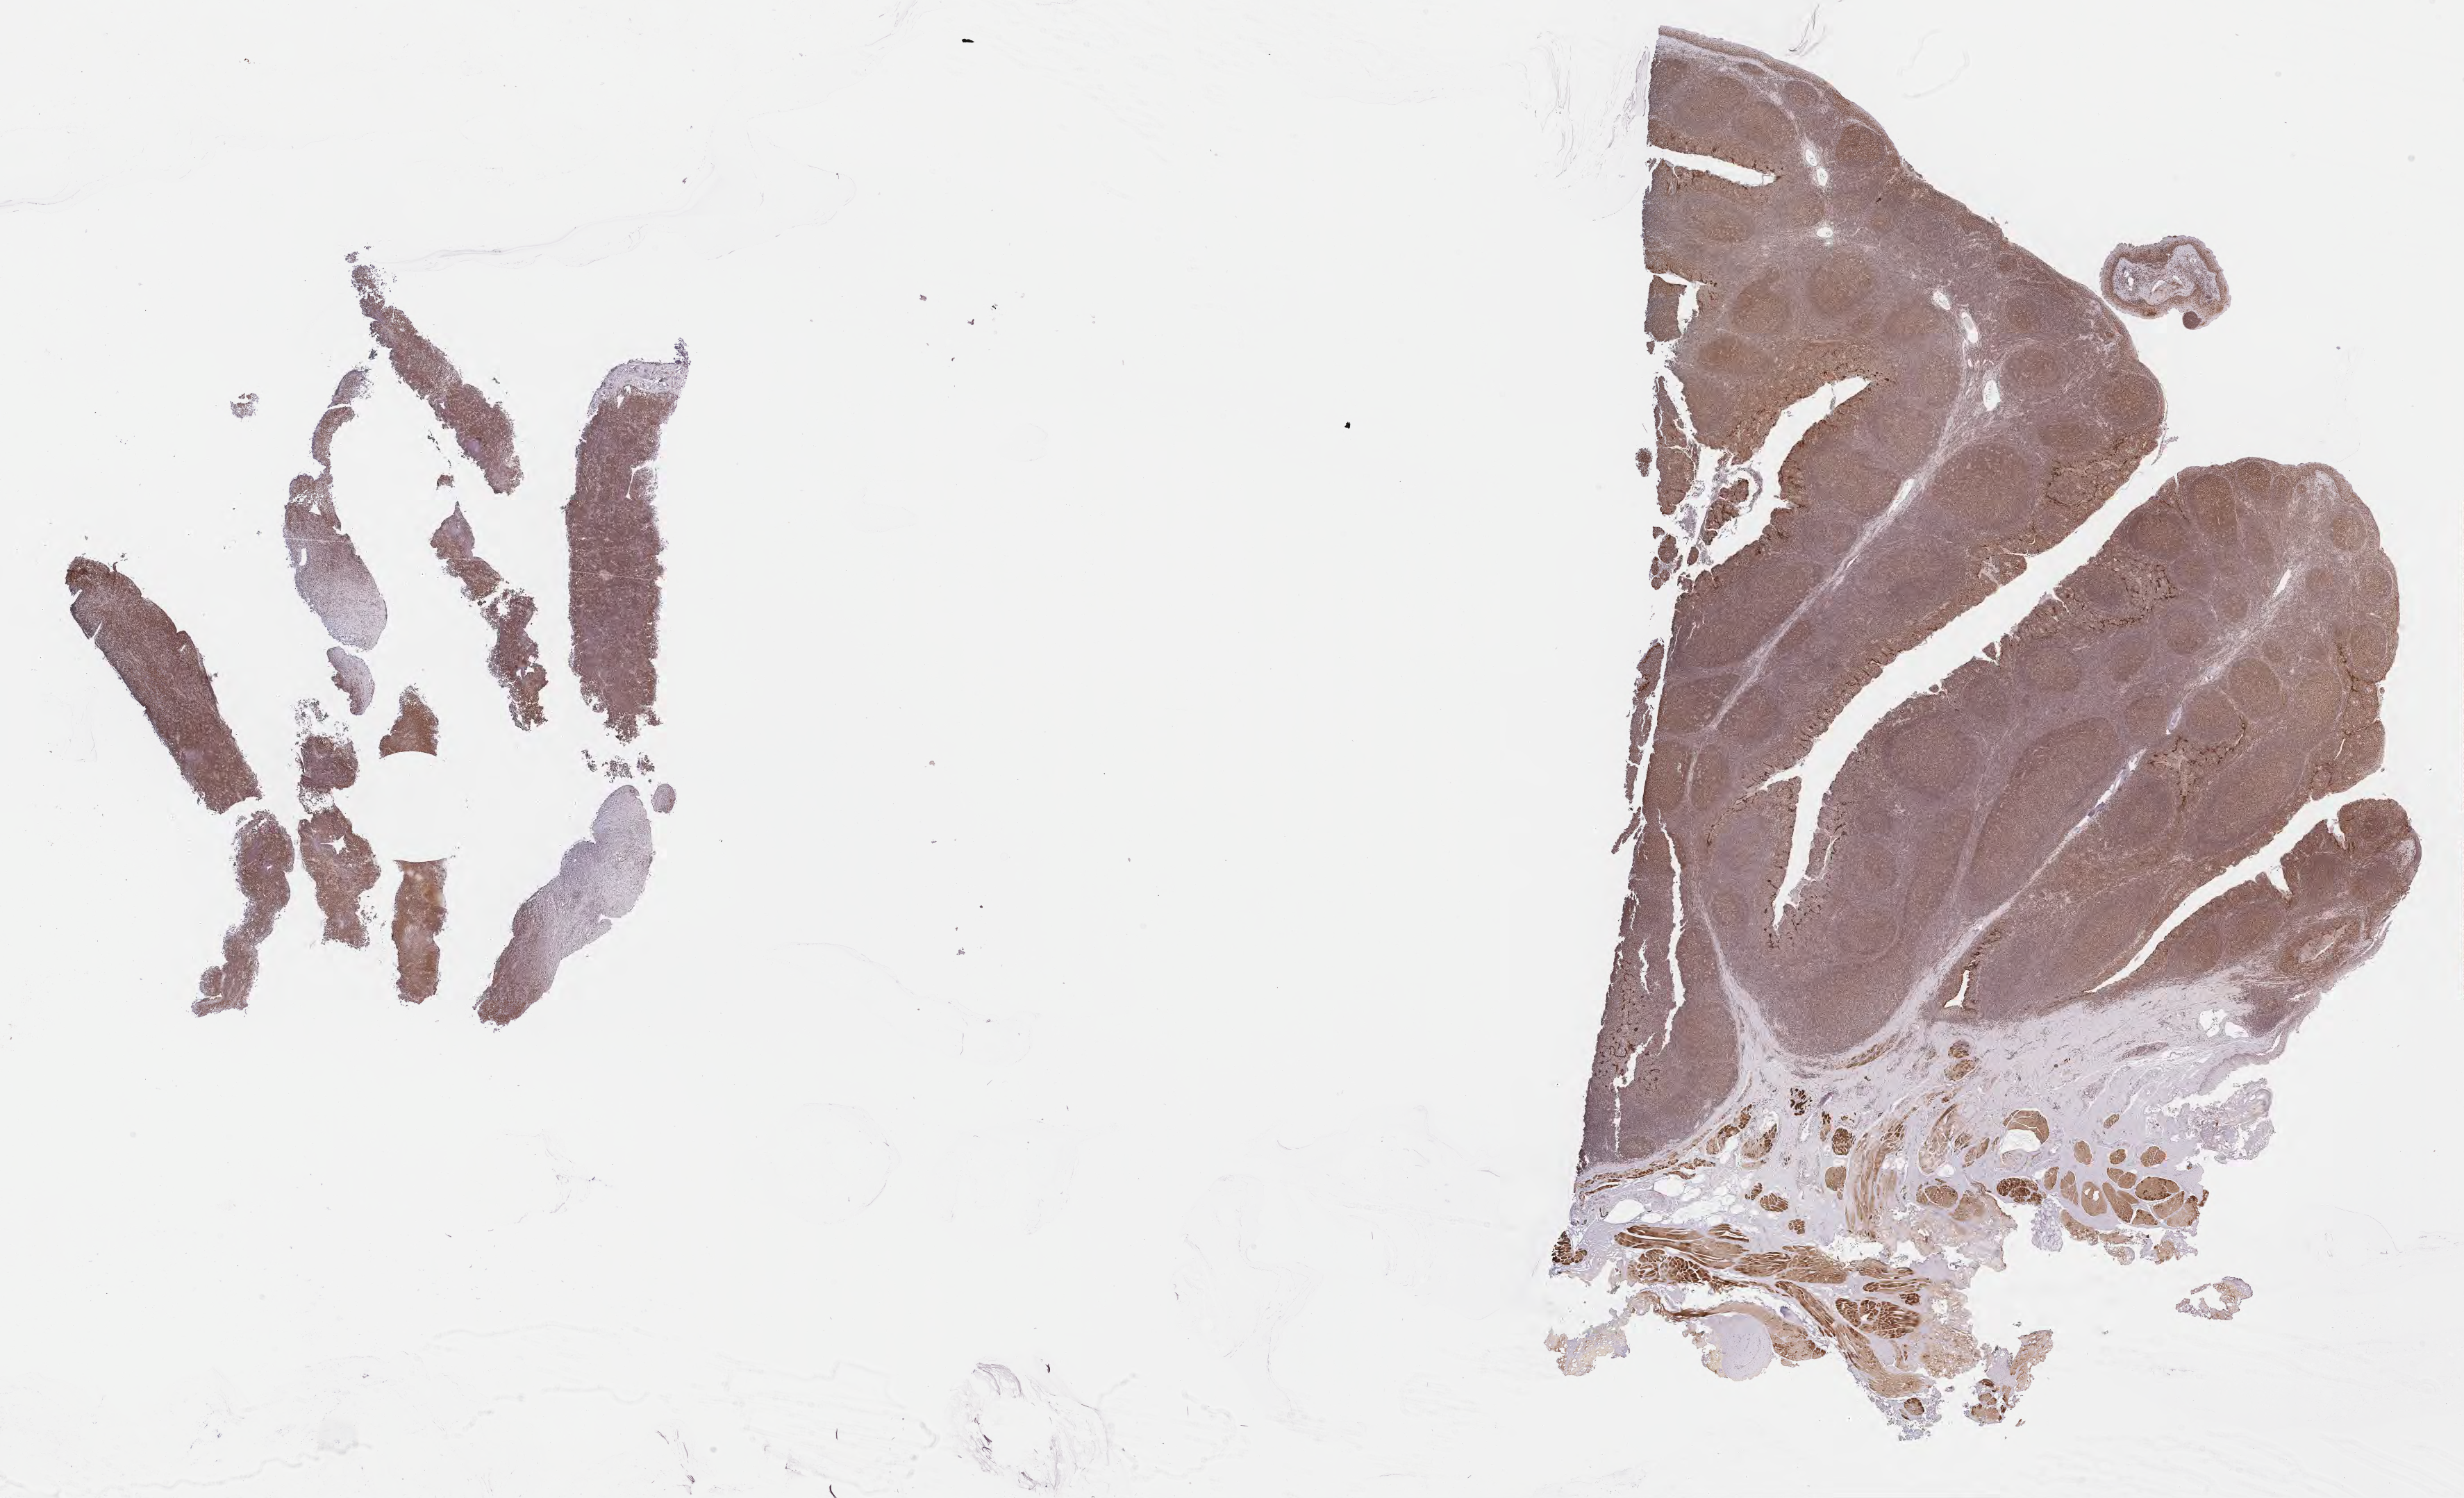
Immunohistochemistry (IHC) whole-slide image stained for BCL6, shown as a low-resolution overview of the whole scanned area (about 28.7 x 17.4 mm), specimen: tumor tissue, site: abdomen proper. Male, age 7 years at initial diagnosis.
* histologic diagnosis: Burkitt lymphoma, NOS